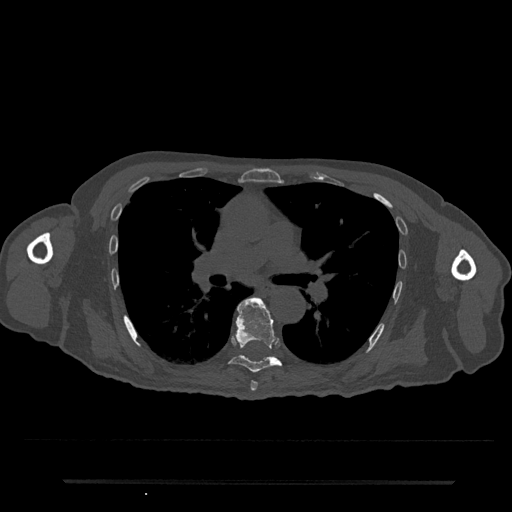
CT including the spine, one axial slice. Slice 484 of 797 in the series (ordered by position). Bone window (W 1800 / L 400 HU). 512 × 512 image matrix. Male patient, age 74 years. From the clinical record (not read from this slice): primary cancer: prostate.
Outlined on this slice (semi-automatic segmentation, software-assisted and operator-edited):
- T6 vertebra: bounding box <250,381,258,391> (left, top, right, bottom; pixels)
- T7 vertebra: <228,297,282,373>